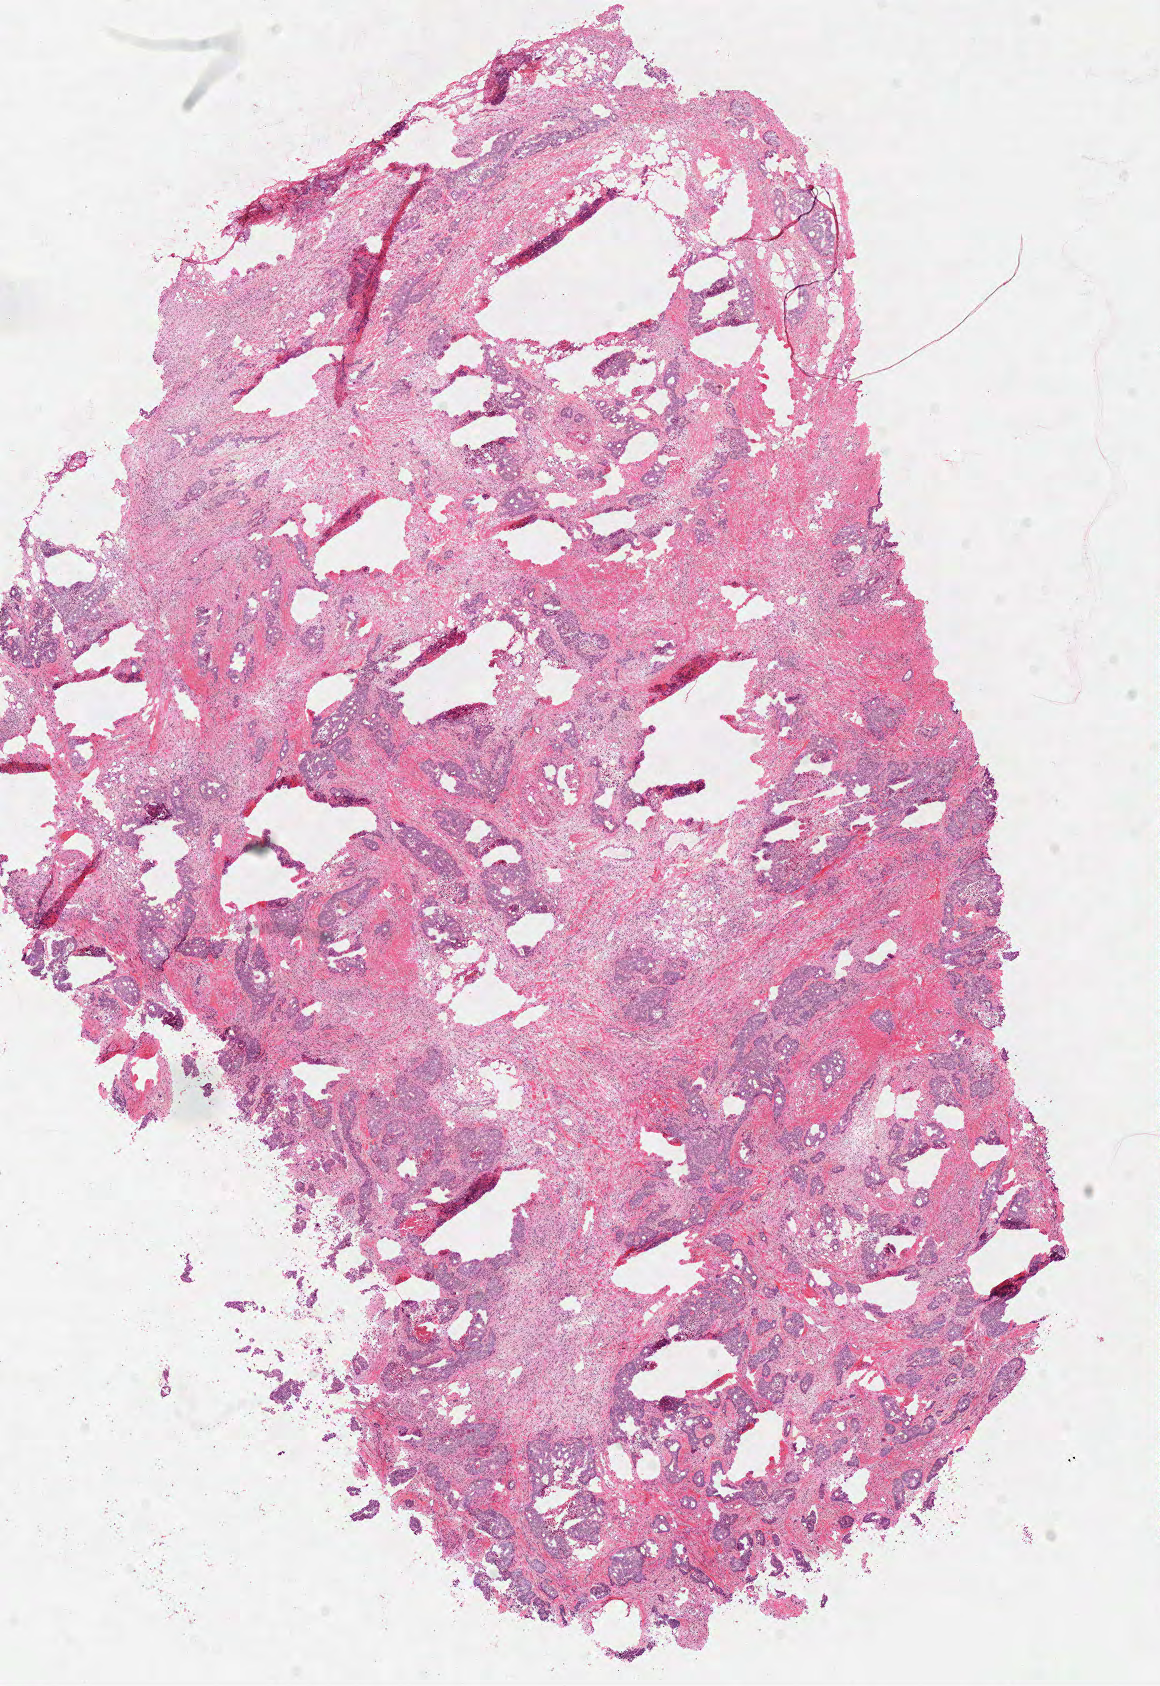
Digitized H&E-stained tissue section (whole slide) — low-resolution overview of the scanned area, about 9.1 x 13.3 mm, frozen section from the top of the tissue portion, sample: primary tumour, rectum. Male, age 62 years at initial diagnosis. Slide review estimates, as recorded: tumour cells 62%, tumour nuclei 60%, normal cells 0%, stromal cells 35%, necrosis 3%.
Pathologic diagnosis: Adenocarcinoma, NOS. AJCC pathologic stage: IVA (7th edition). Lymph nodes positive (case pathology): 7 of 22 examined.